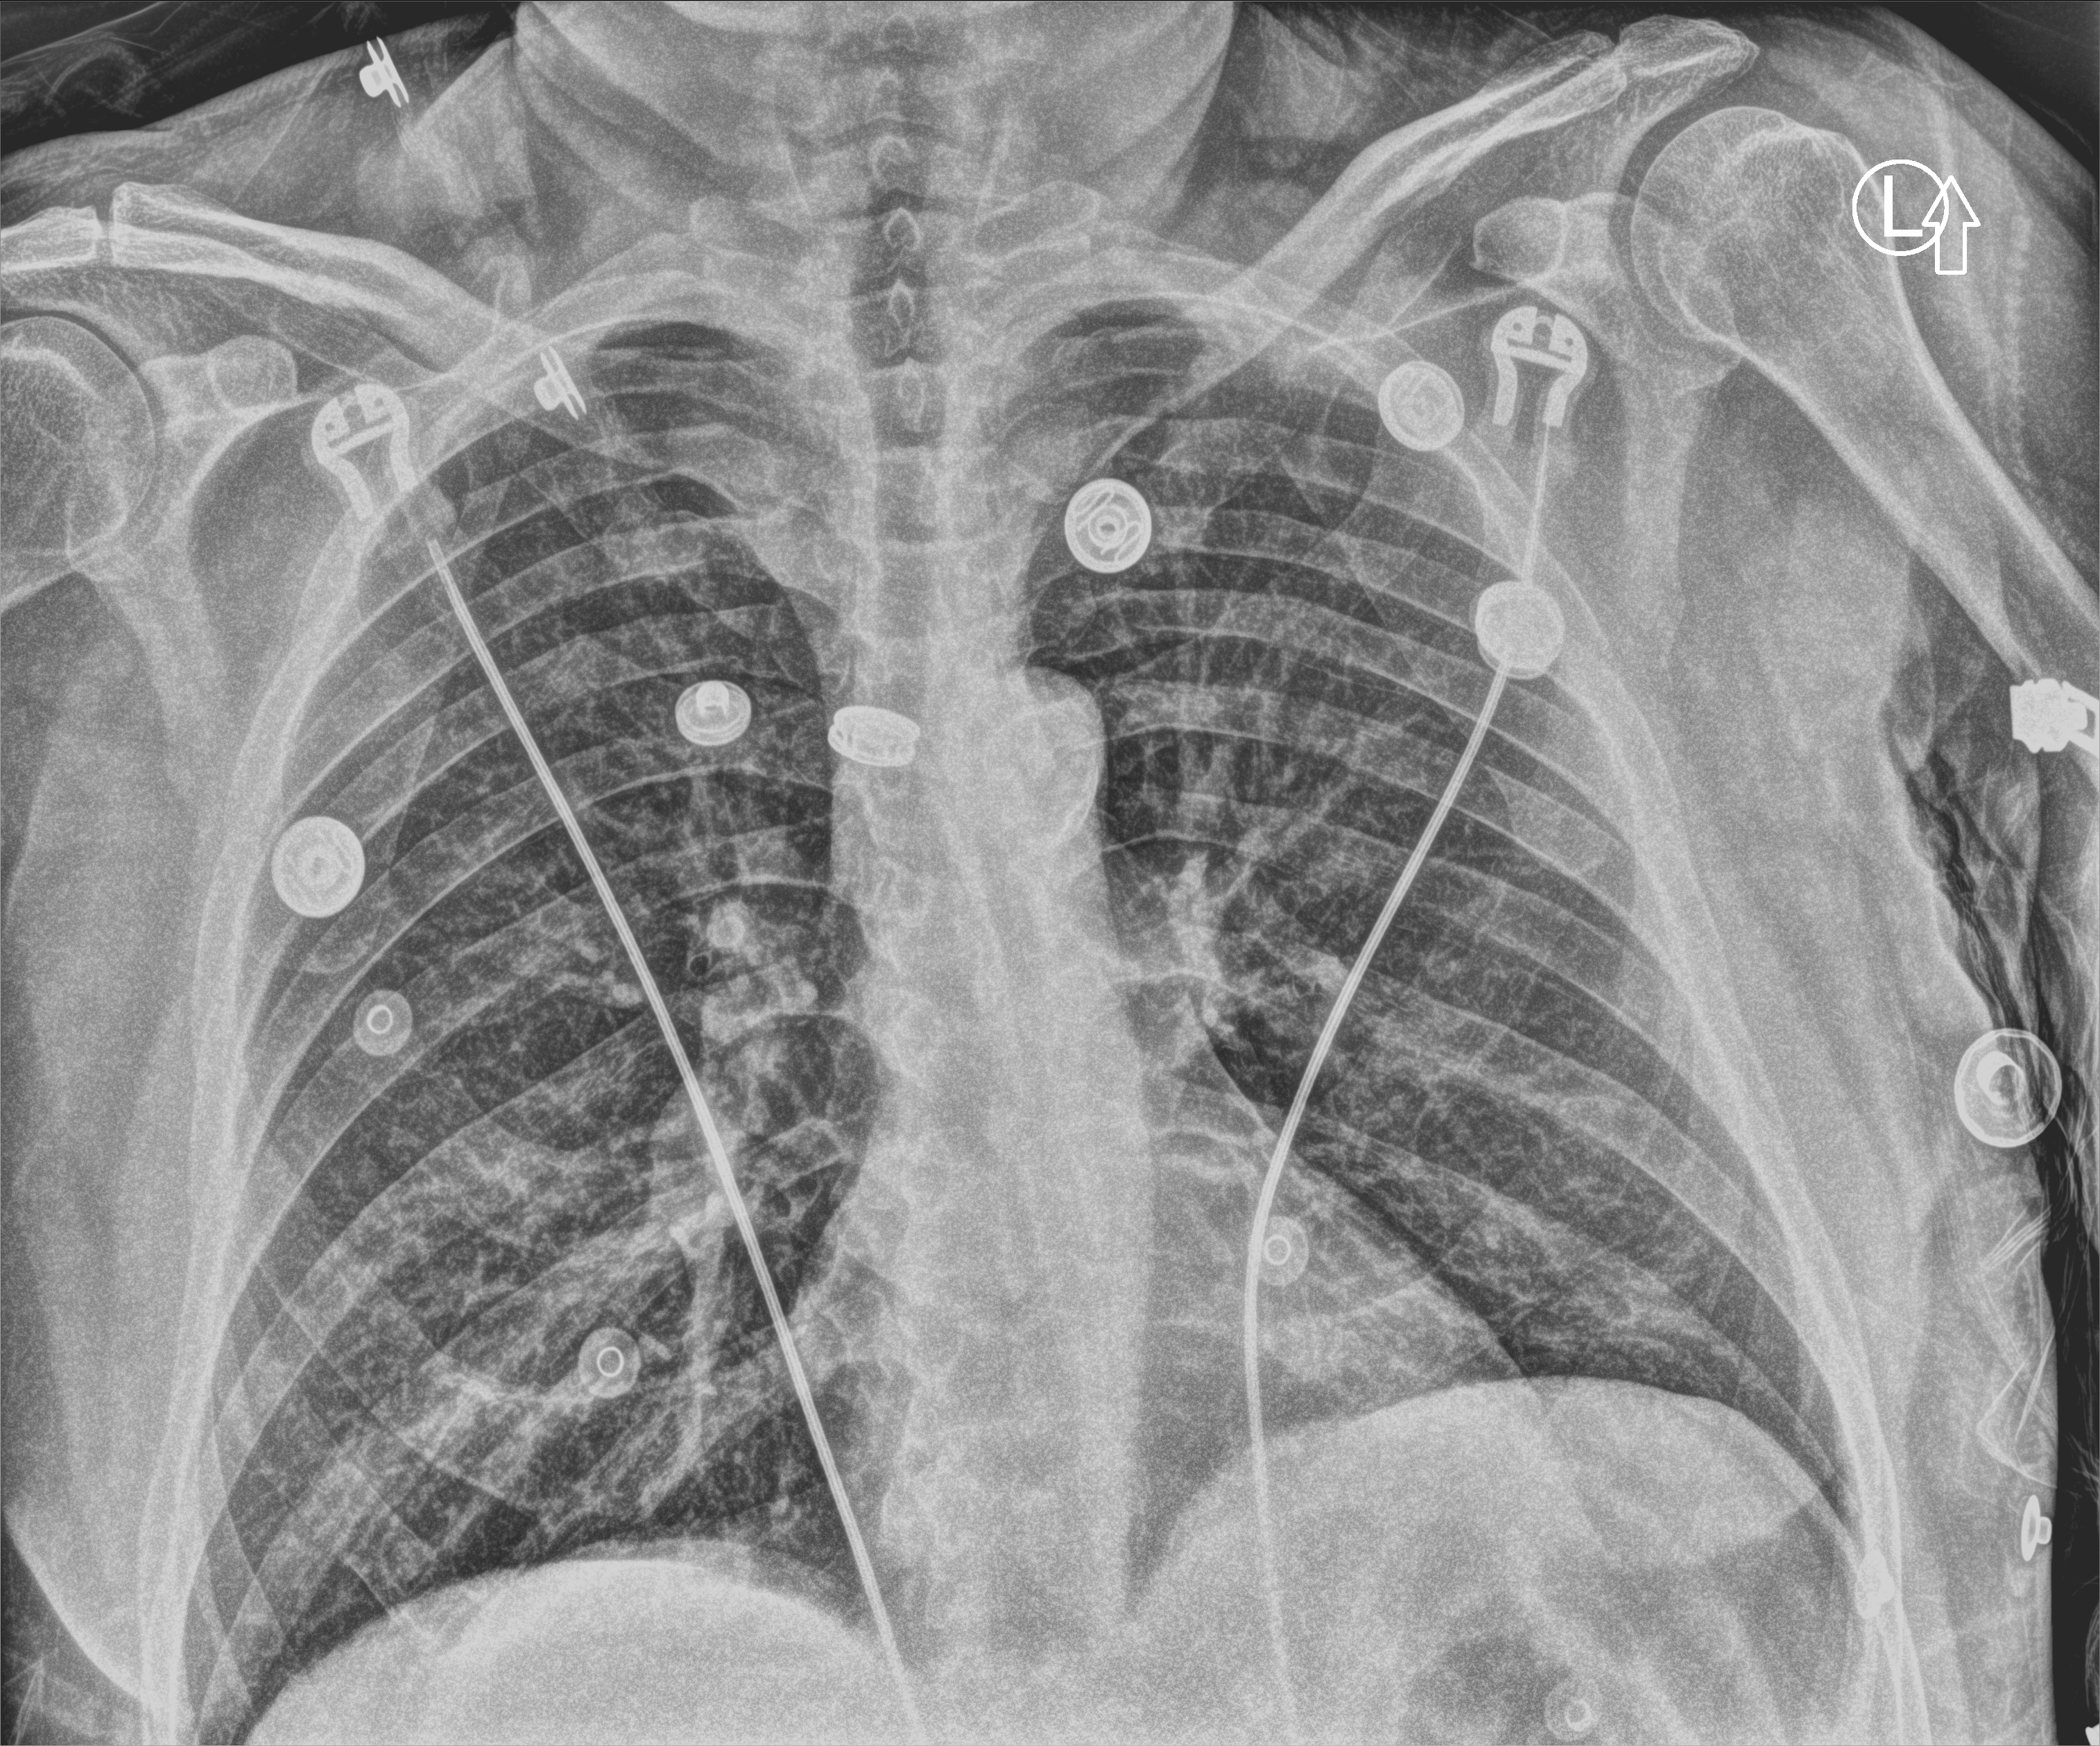
Chest X-ray (portable), anteroposterior (AP) projection. Patient hospitalised with COVID-19; male, aged 18–59 years.
From the hospital-stay record, not from the radiograph (when in the stay this image was taken is not recorded): mechanically ventilated during this hospital stay: no.